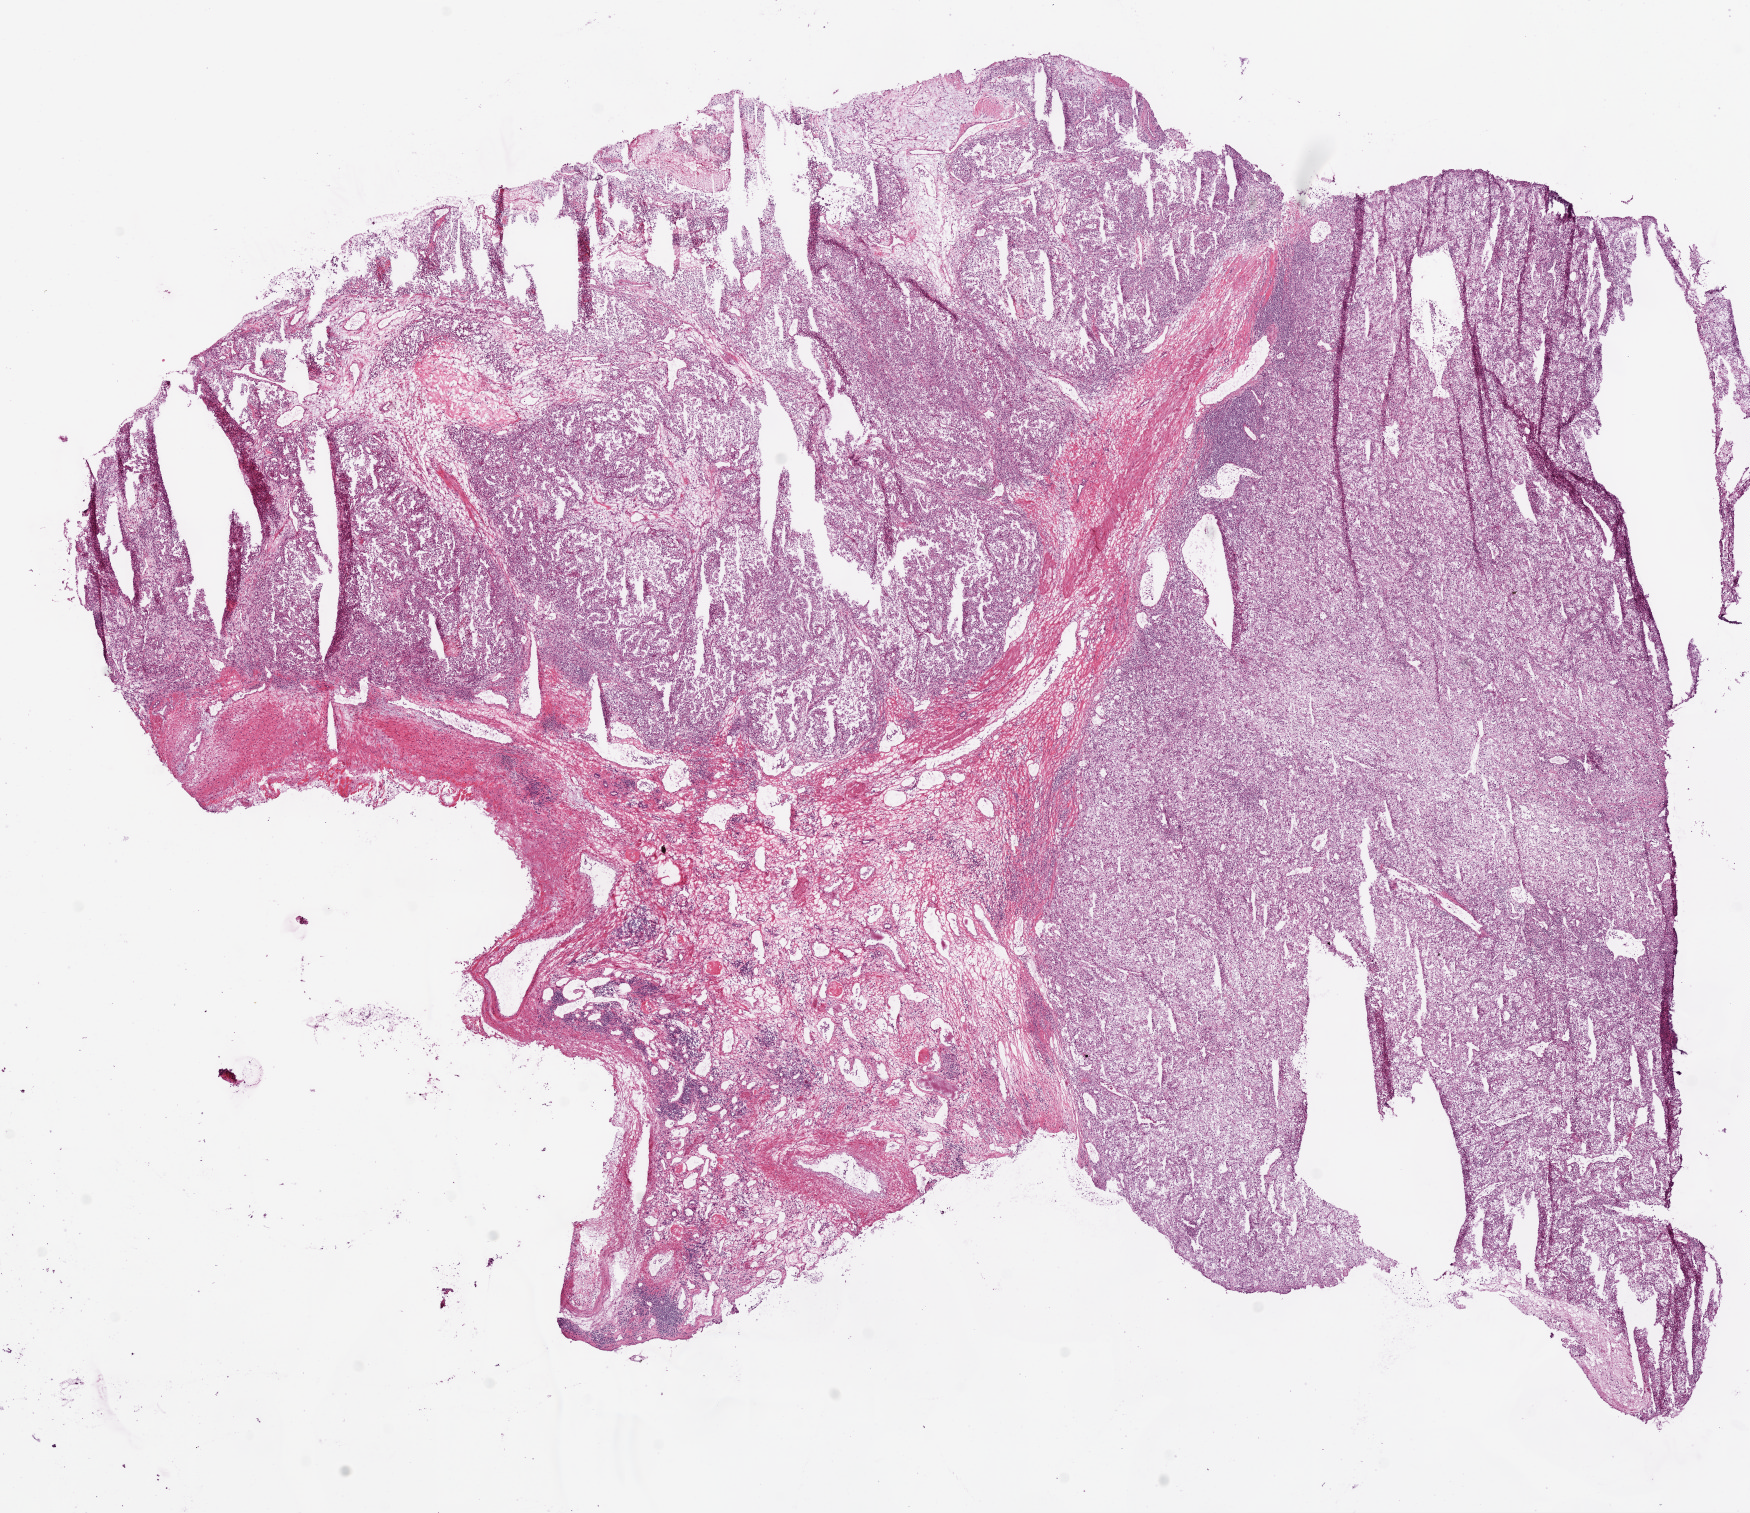
Whole-slide histology image, H&E — shown as a low-resolution overview of the whole scanned area (about 14.0 x 12.1 mm), frozen section from the bottom of the tissue portion, kidney, primary tumour sample. Male patient; age at initial diagnosis 47 years. Histologic grade: G3 (poorly differentiated). Pathologist review of this section (percent, as recorded): tumour cells 85%, tumour nuclei 75%, normal cells 0%, stromal cells 15%, necrosis 0%.
Lymph nodes positive (case pathology): 0 of 5 examined. Histologic diagnosis: Clear cell adenocarcinoma, NOS. TNM: T2 N0 M0. AJCC pathologic stage: II.